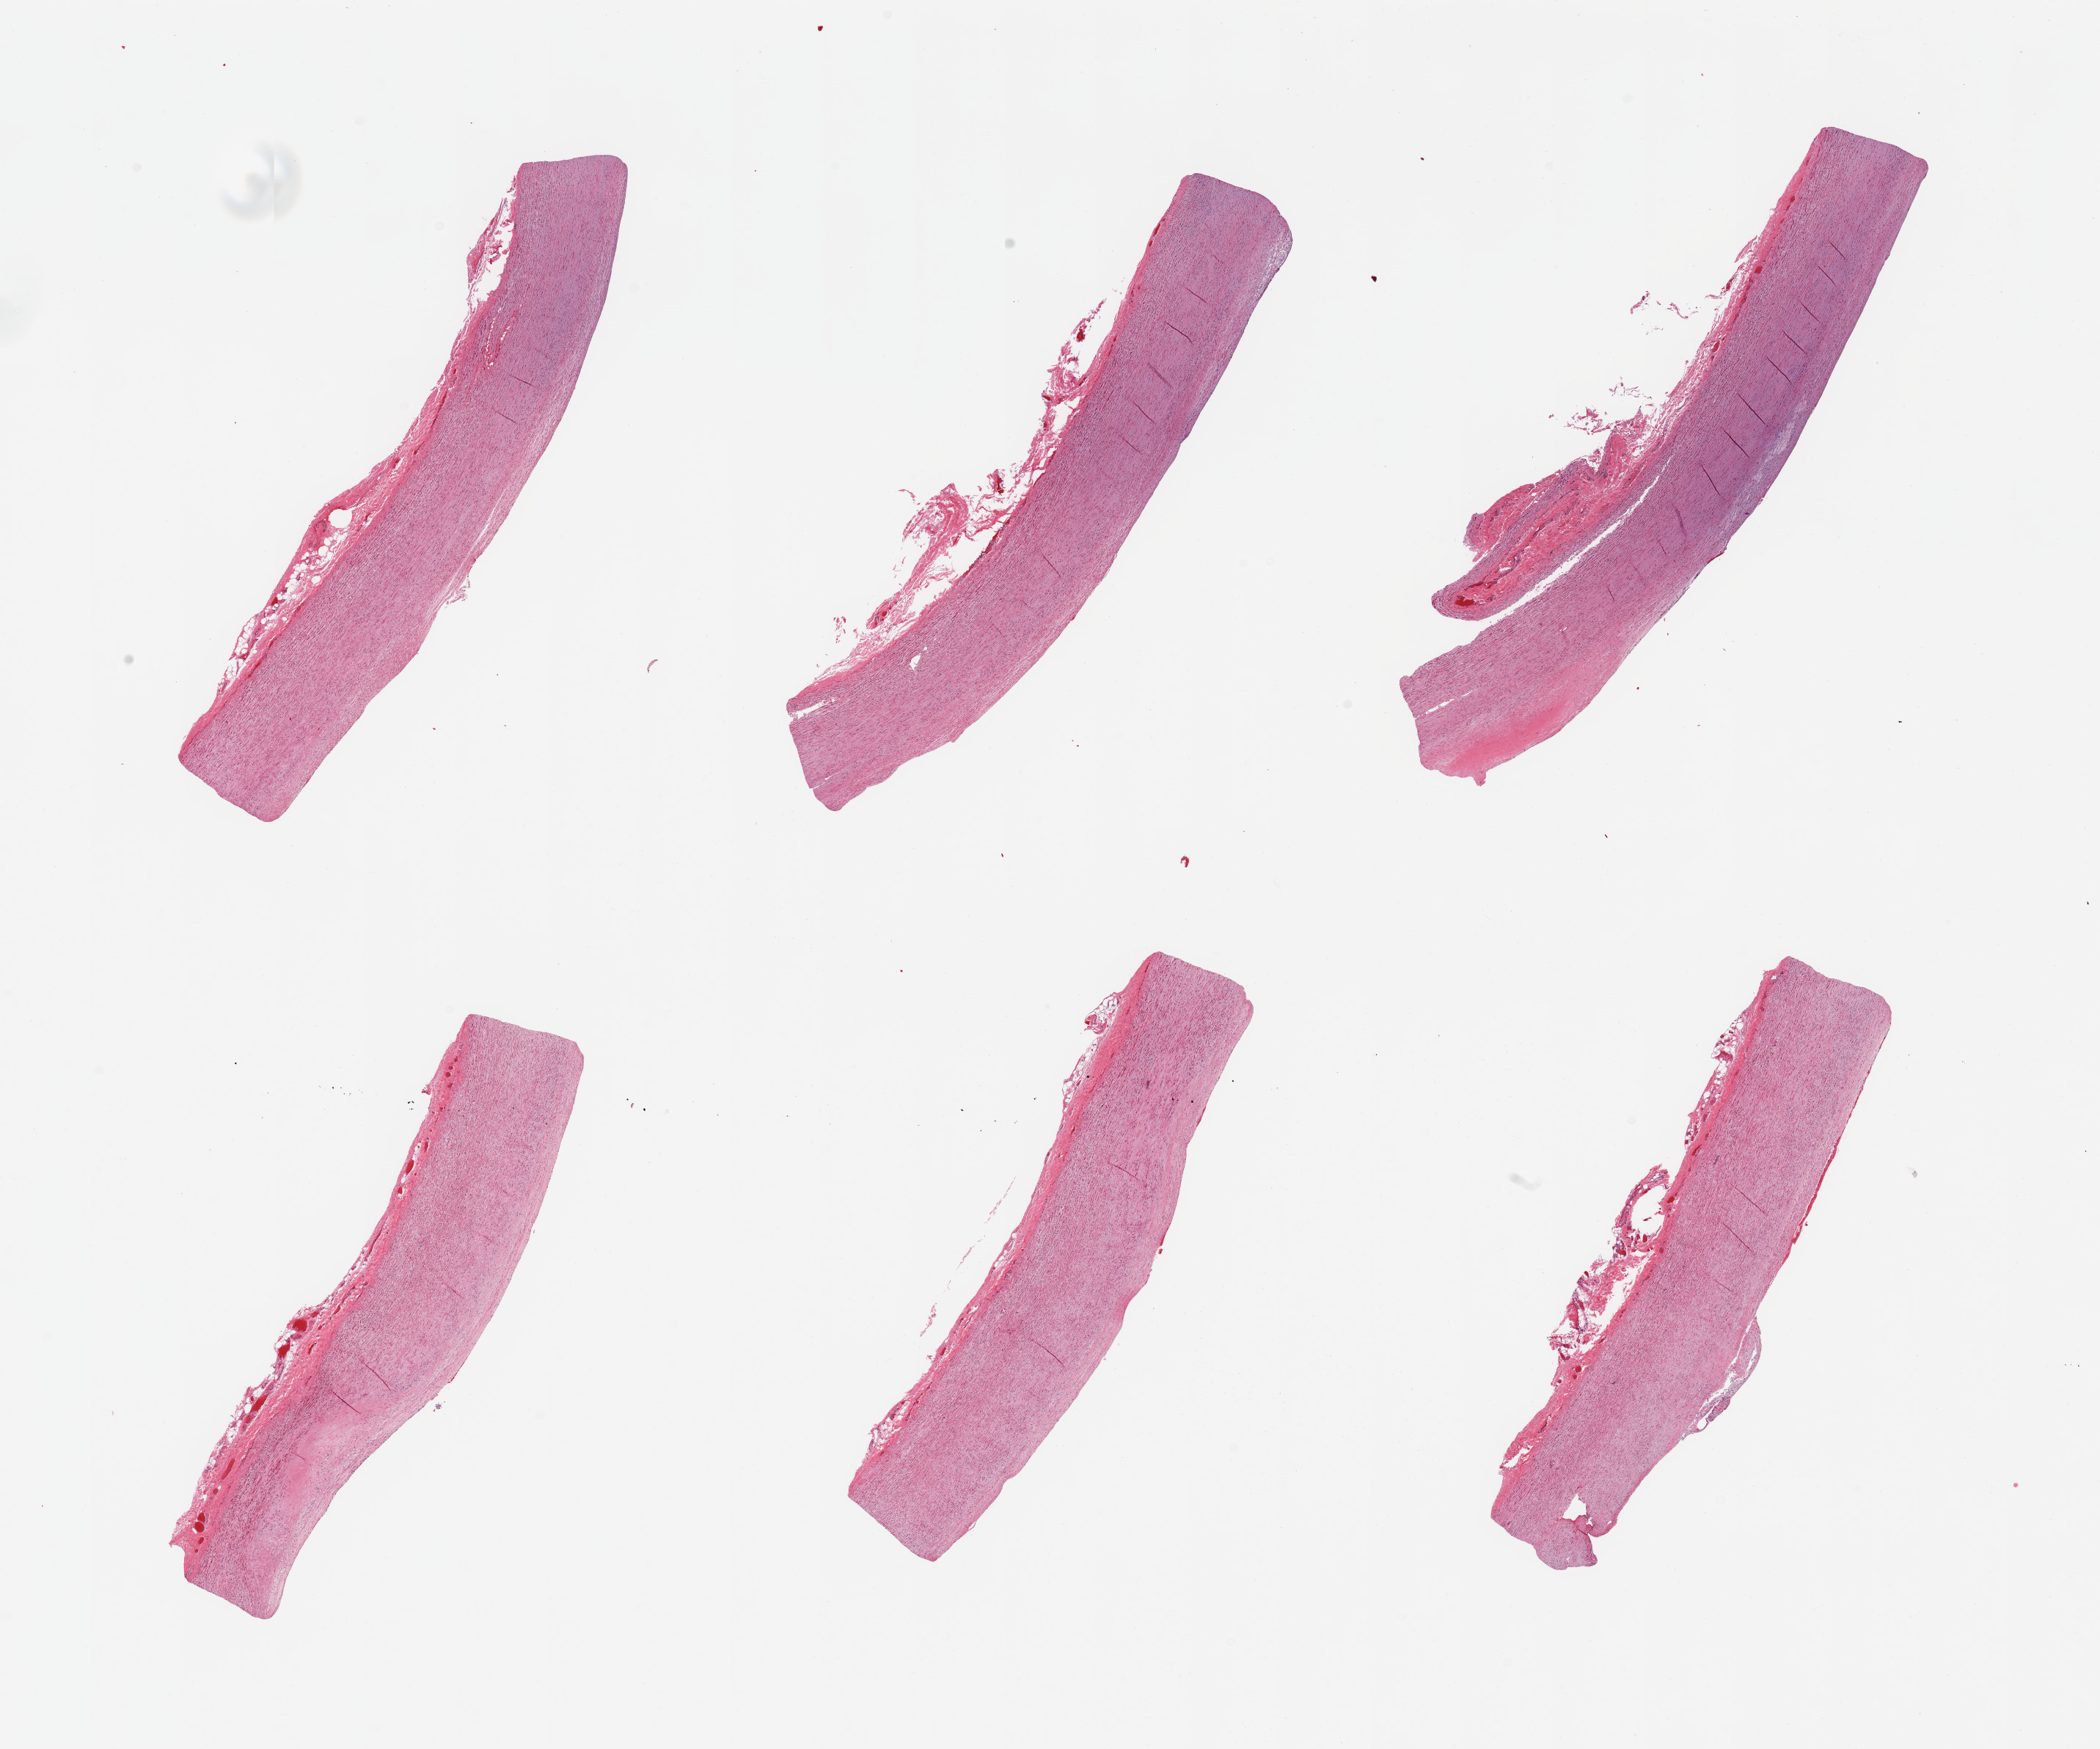
Digitized hematoxylin and eosin (H&E)-stained section, whole scanned area (about 22.6 x 18.9 mm, acquisition: 20x scan) shown as a low-resolution overview, PAXgene-fixed paraffin-embedded (PFPE) section, section of aorta (target tissue), donor tissue sample. Donor sex: male.
Review note (as recorded): 6 pieces; atherosclerosis.